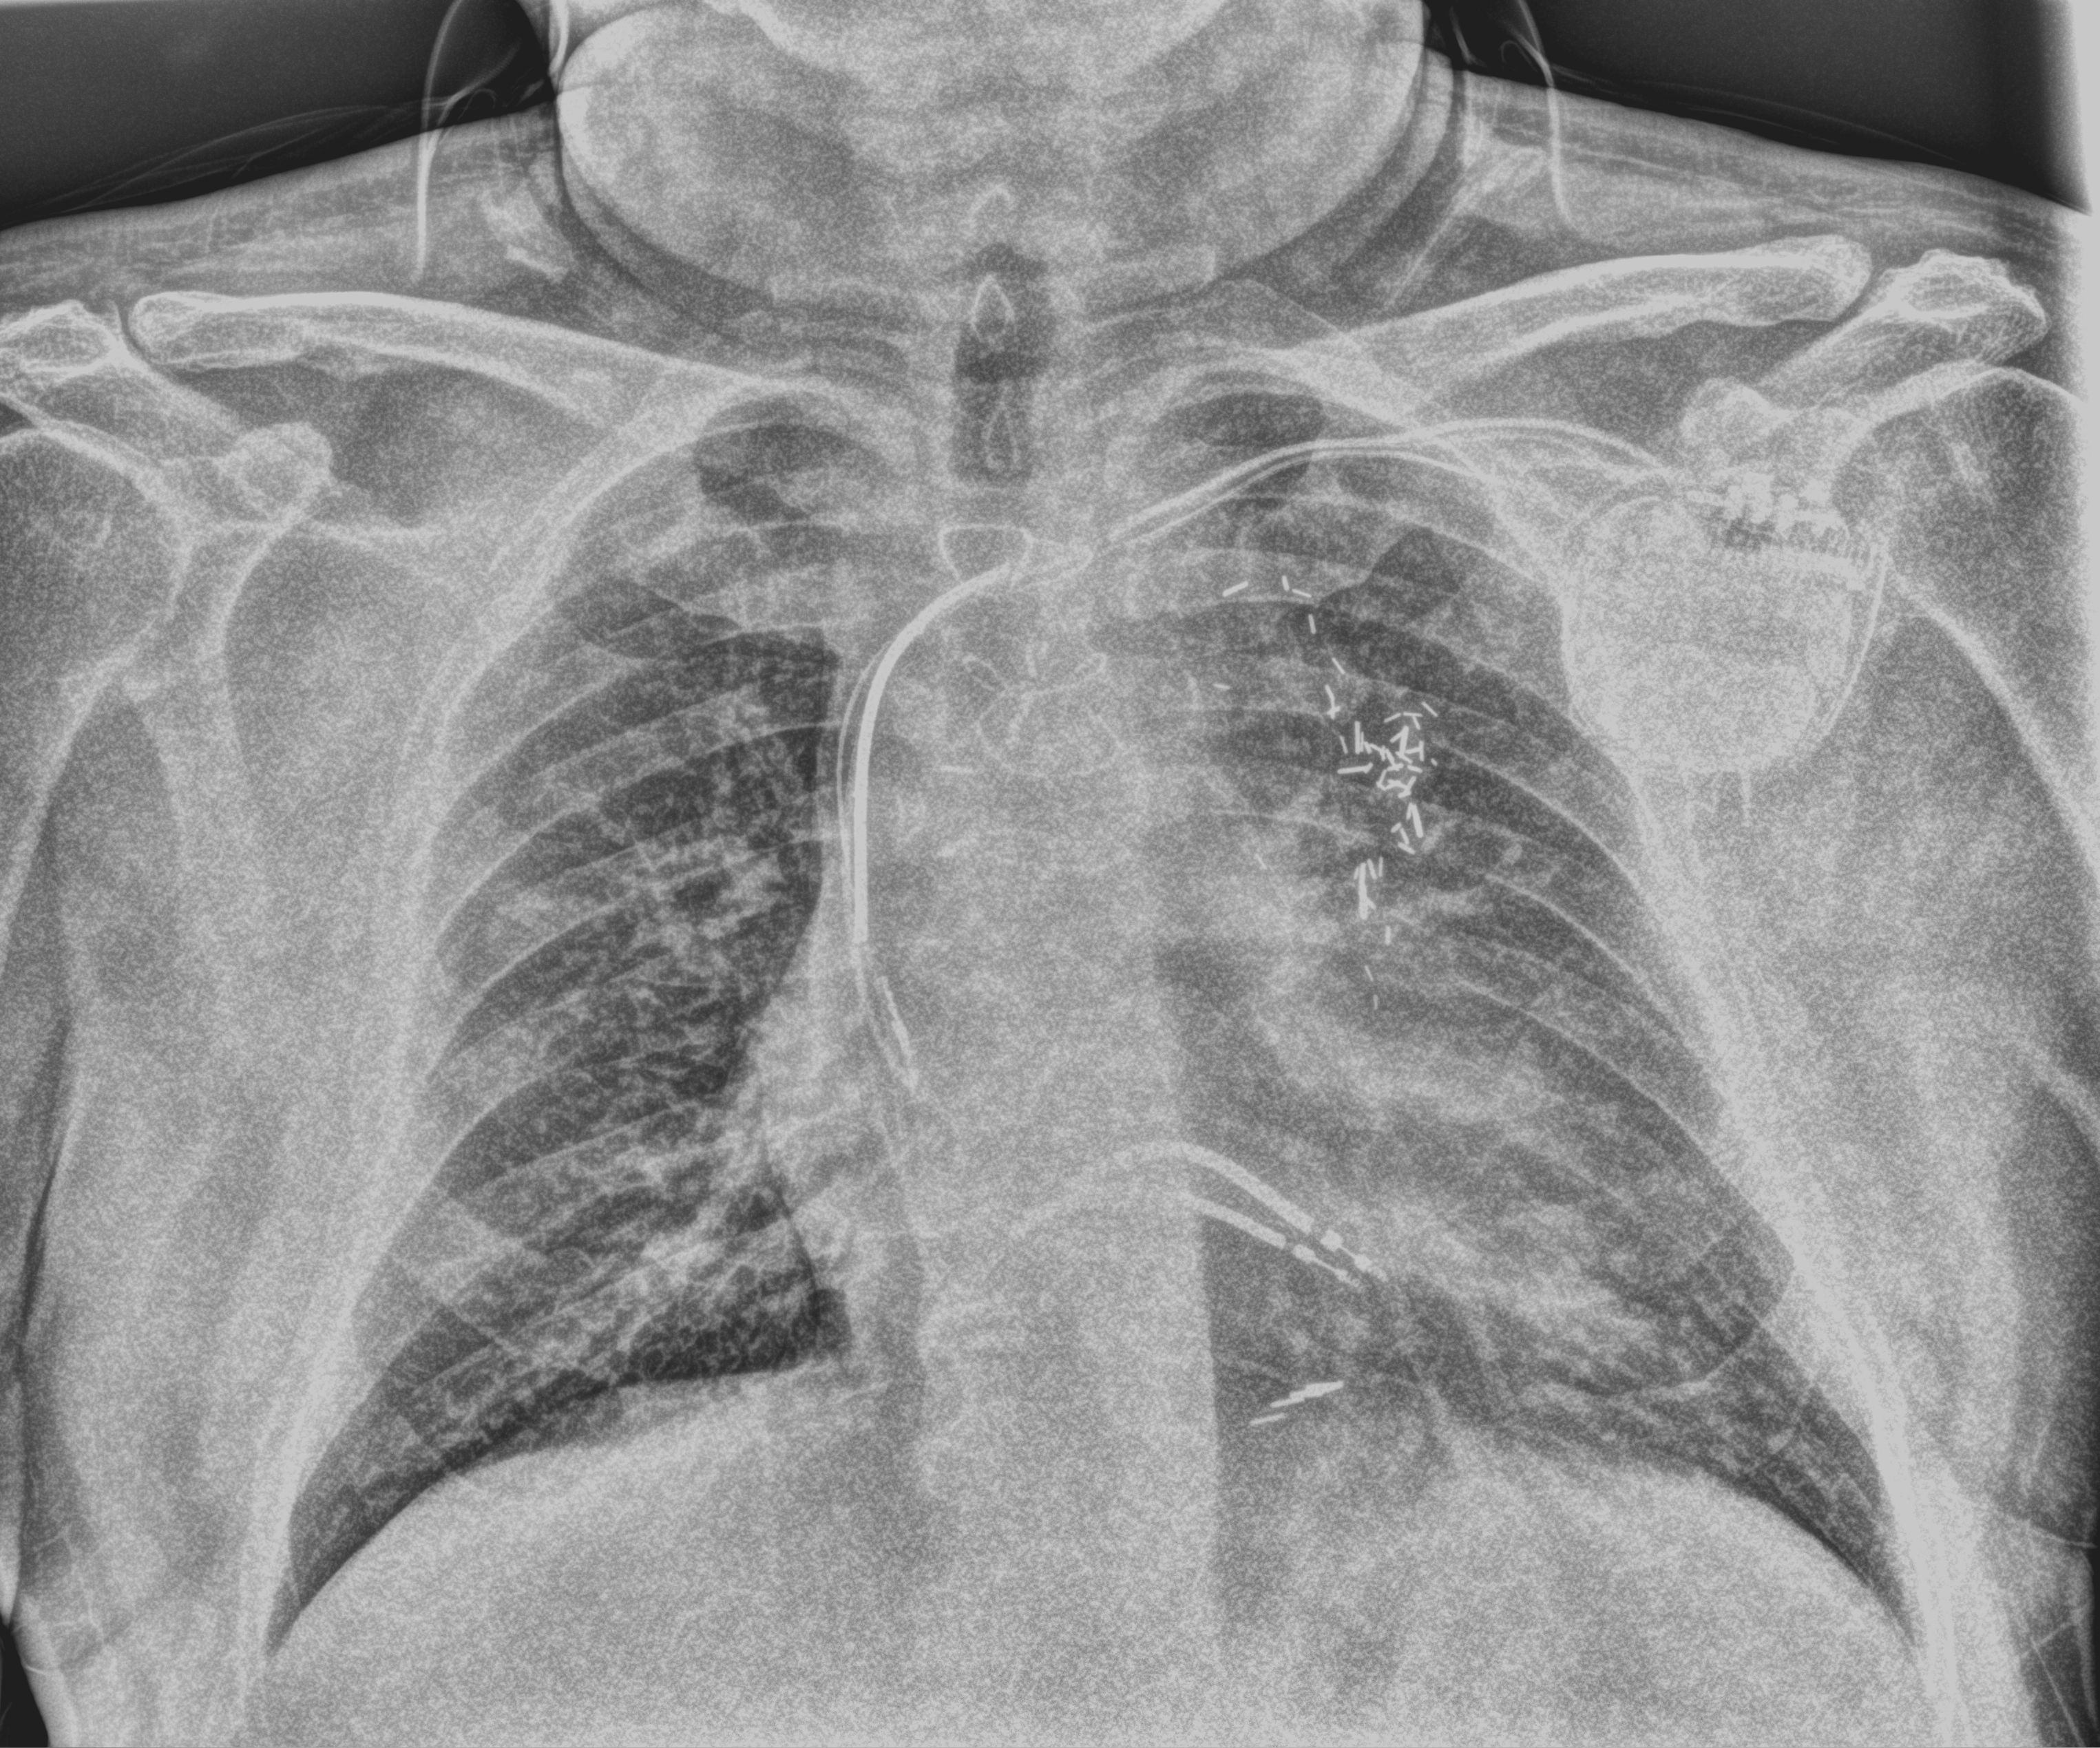
Bedside chest radiograph (computed radiography). Male patient hospitalised with COVID-19, age 60–74 years.
Hospital-stay facts (about this admission, not read from this image; timing relative to this image not recorded):
- diabetes (admission record): yes
- smoking status (admission record): never
- mechanically ventilated during this hospital stay: yes